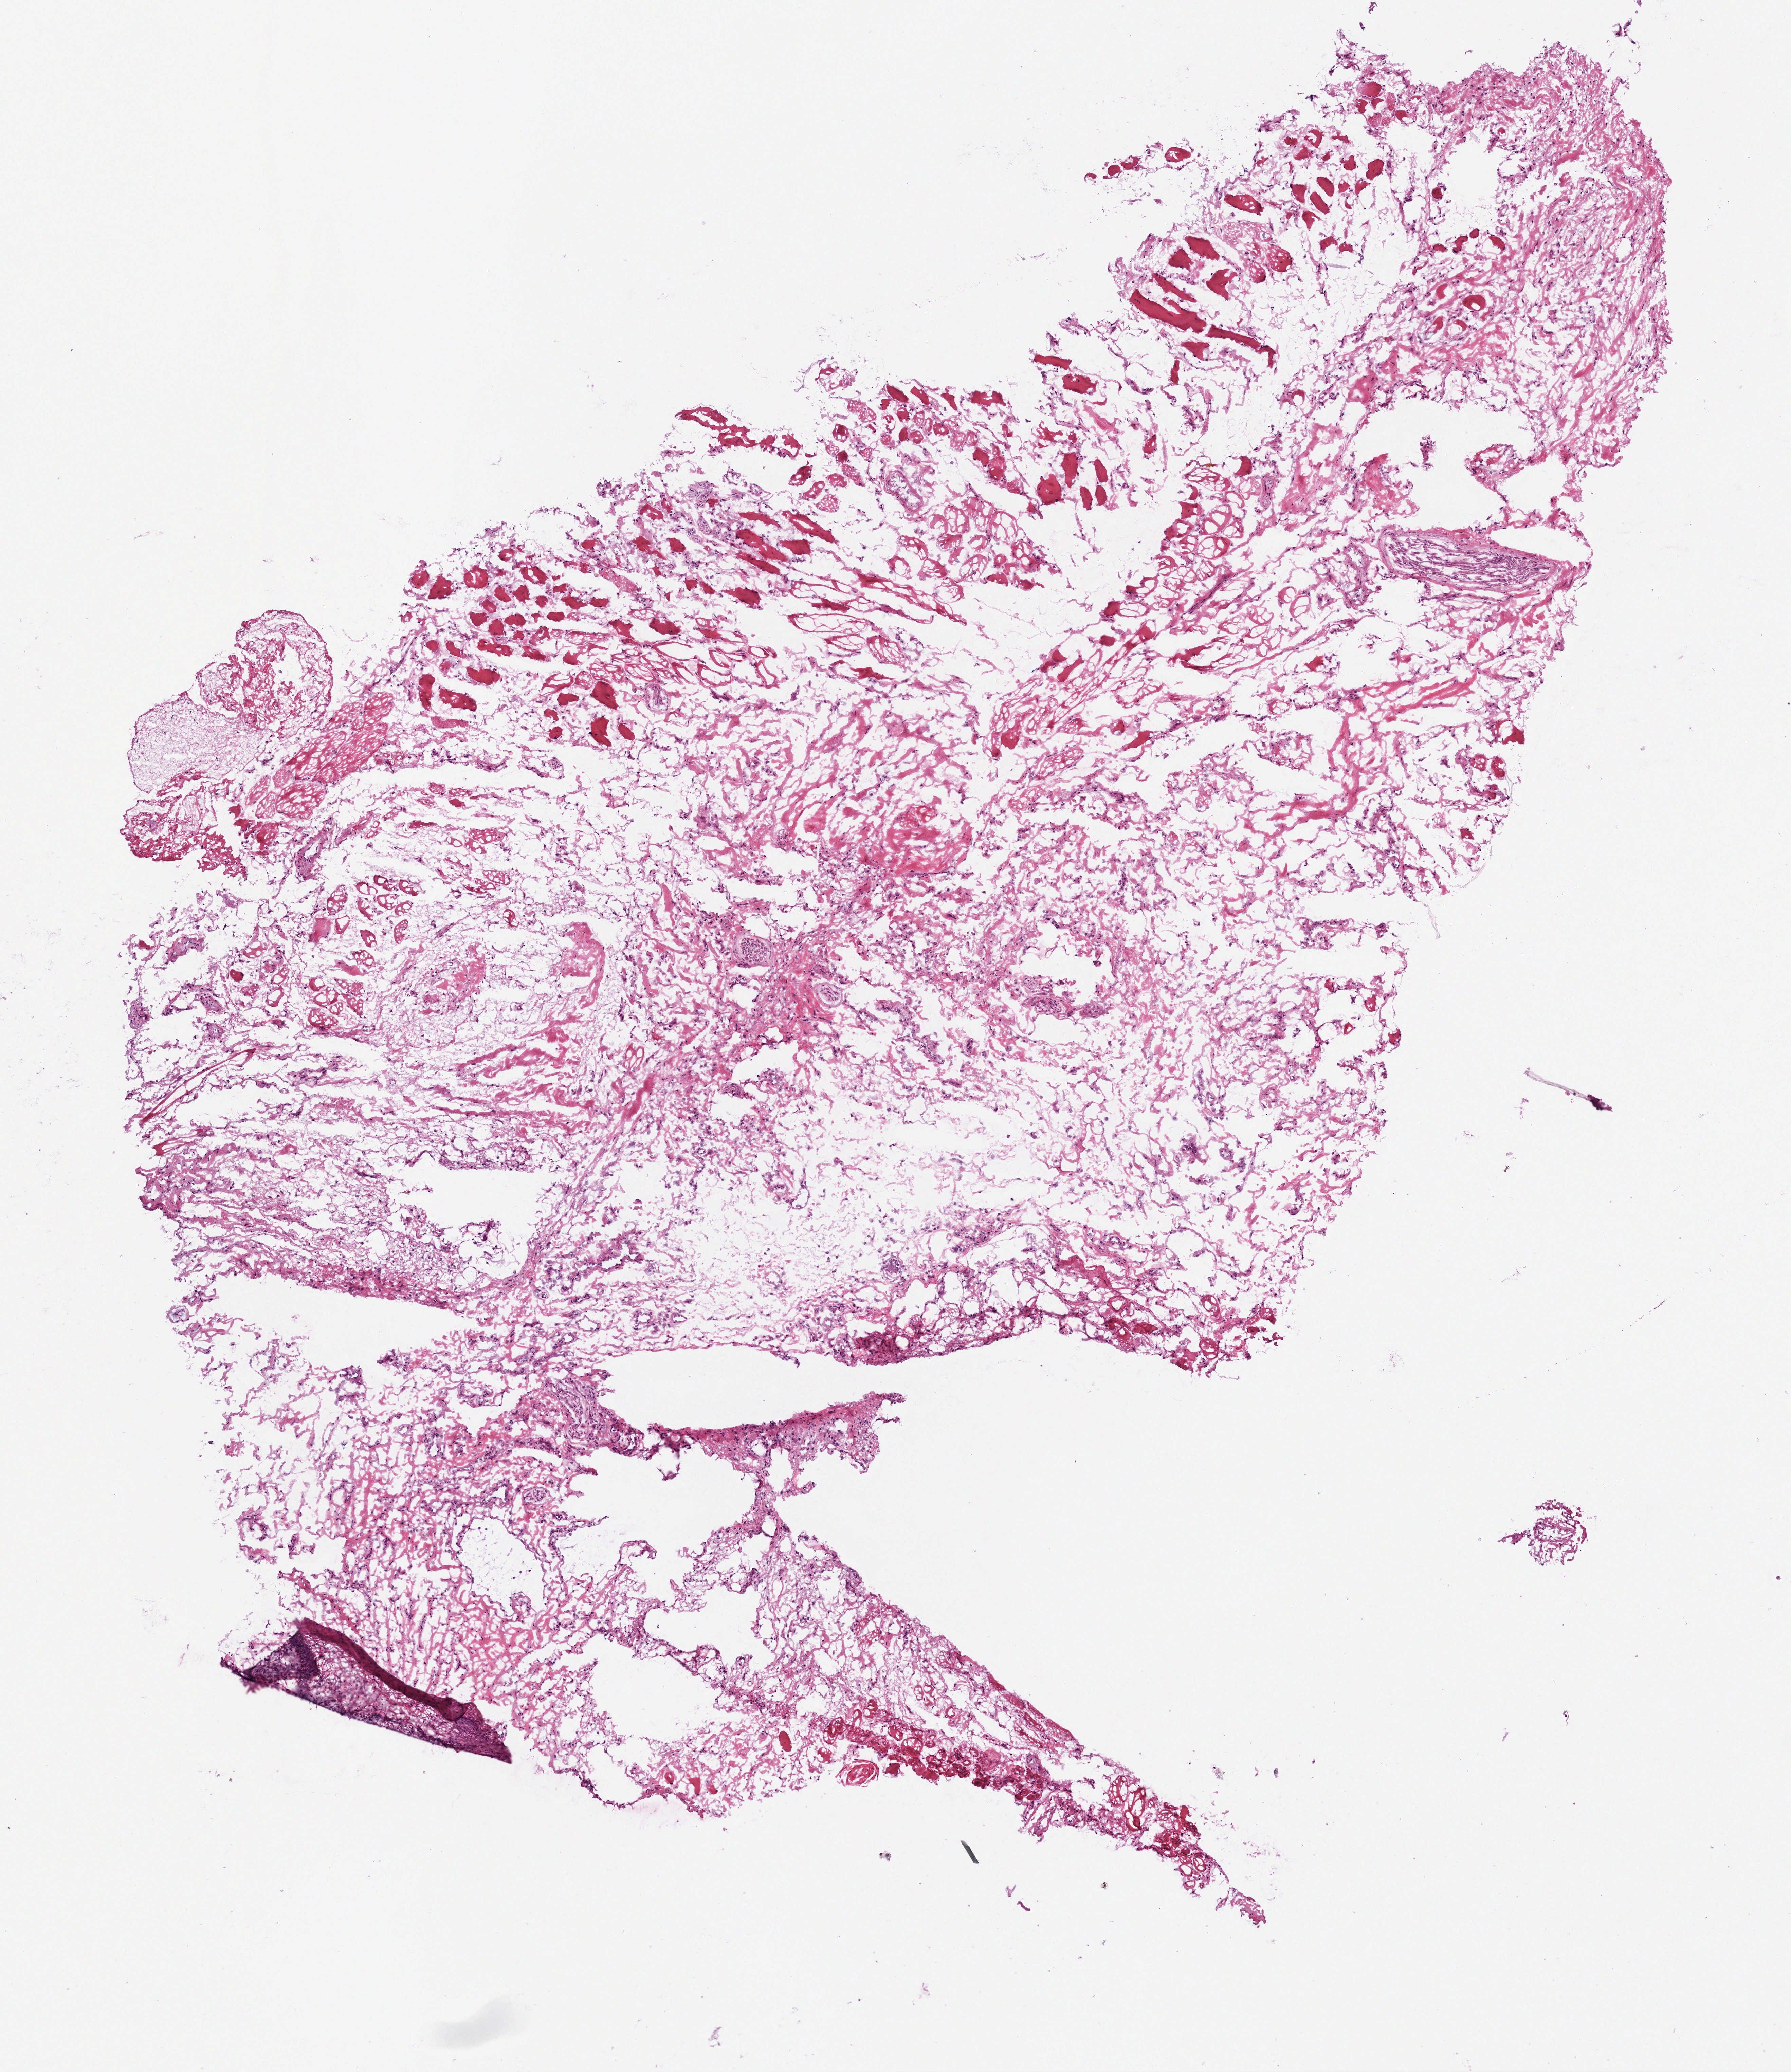
Whole-slide histology image, H&E-stained — shown as a low-resolution overview of the whole scanned area (about 5.3 x 6.2 mm), frozen section, head and neck, solid tissue normal (non-tumour tissue) sample. Female, age 79 years at initial diagnosis. Composition of this section per pathologist review: tumour cells 0%, tumour nuclei 0%, normal cells 100%, stromal cells 0%, necrosis 0%. Infiltration values recorded for this section: lymphocyte infiltration 0%, monocyte infiltration 0%, neutrophil infiltration 0%.
This section: solid tissue normal sample (biorepository sample class). Patient diagnosis: Squamous cell carcinoma, NOS (tongue, NOS).